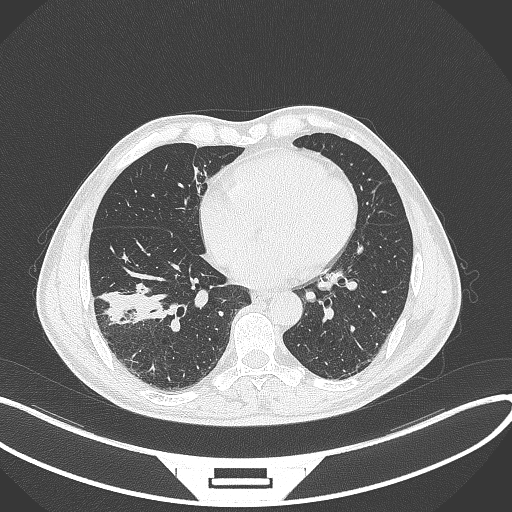
Chest CT, one axial slice; position 138 of 364 along the scan axis; reconstruction kernel B70f; 120 kVp; lung window (W 1500 / L -600 HU); 1 mm slice thickness; 512 × 512 image matrix. Male patient, age 58 years. From the clinical record (not read from this slice): clinical TNM (as recorded): T3 N0 M0; histopathological grade: G2.
Outlined on this slice (rectangle marked by the reading radiologist):
- lung tumour (recorded histology: squamous cell carcinoma): bounding box [x1, y1, x2, y2] px = [96, 289, 168, 328]